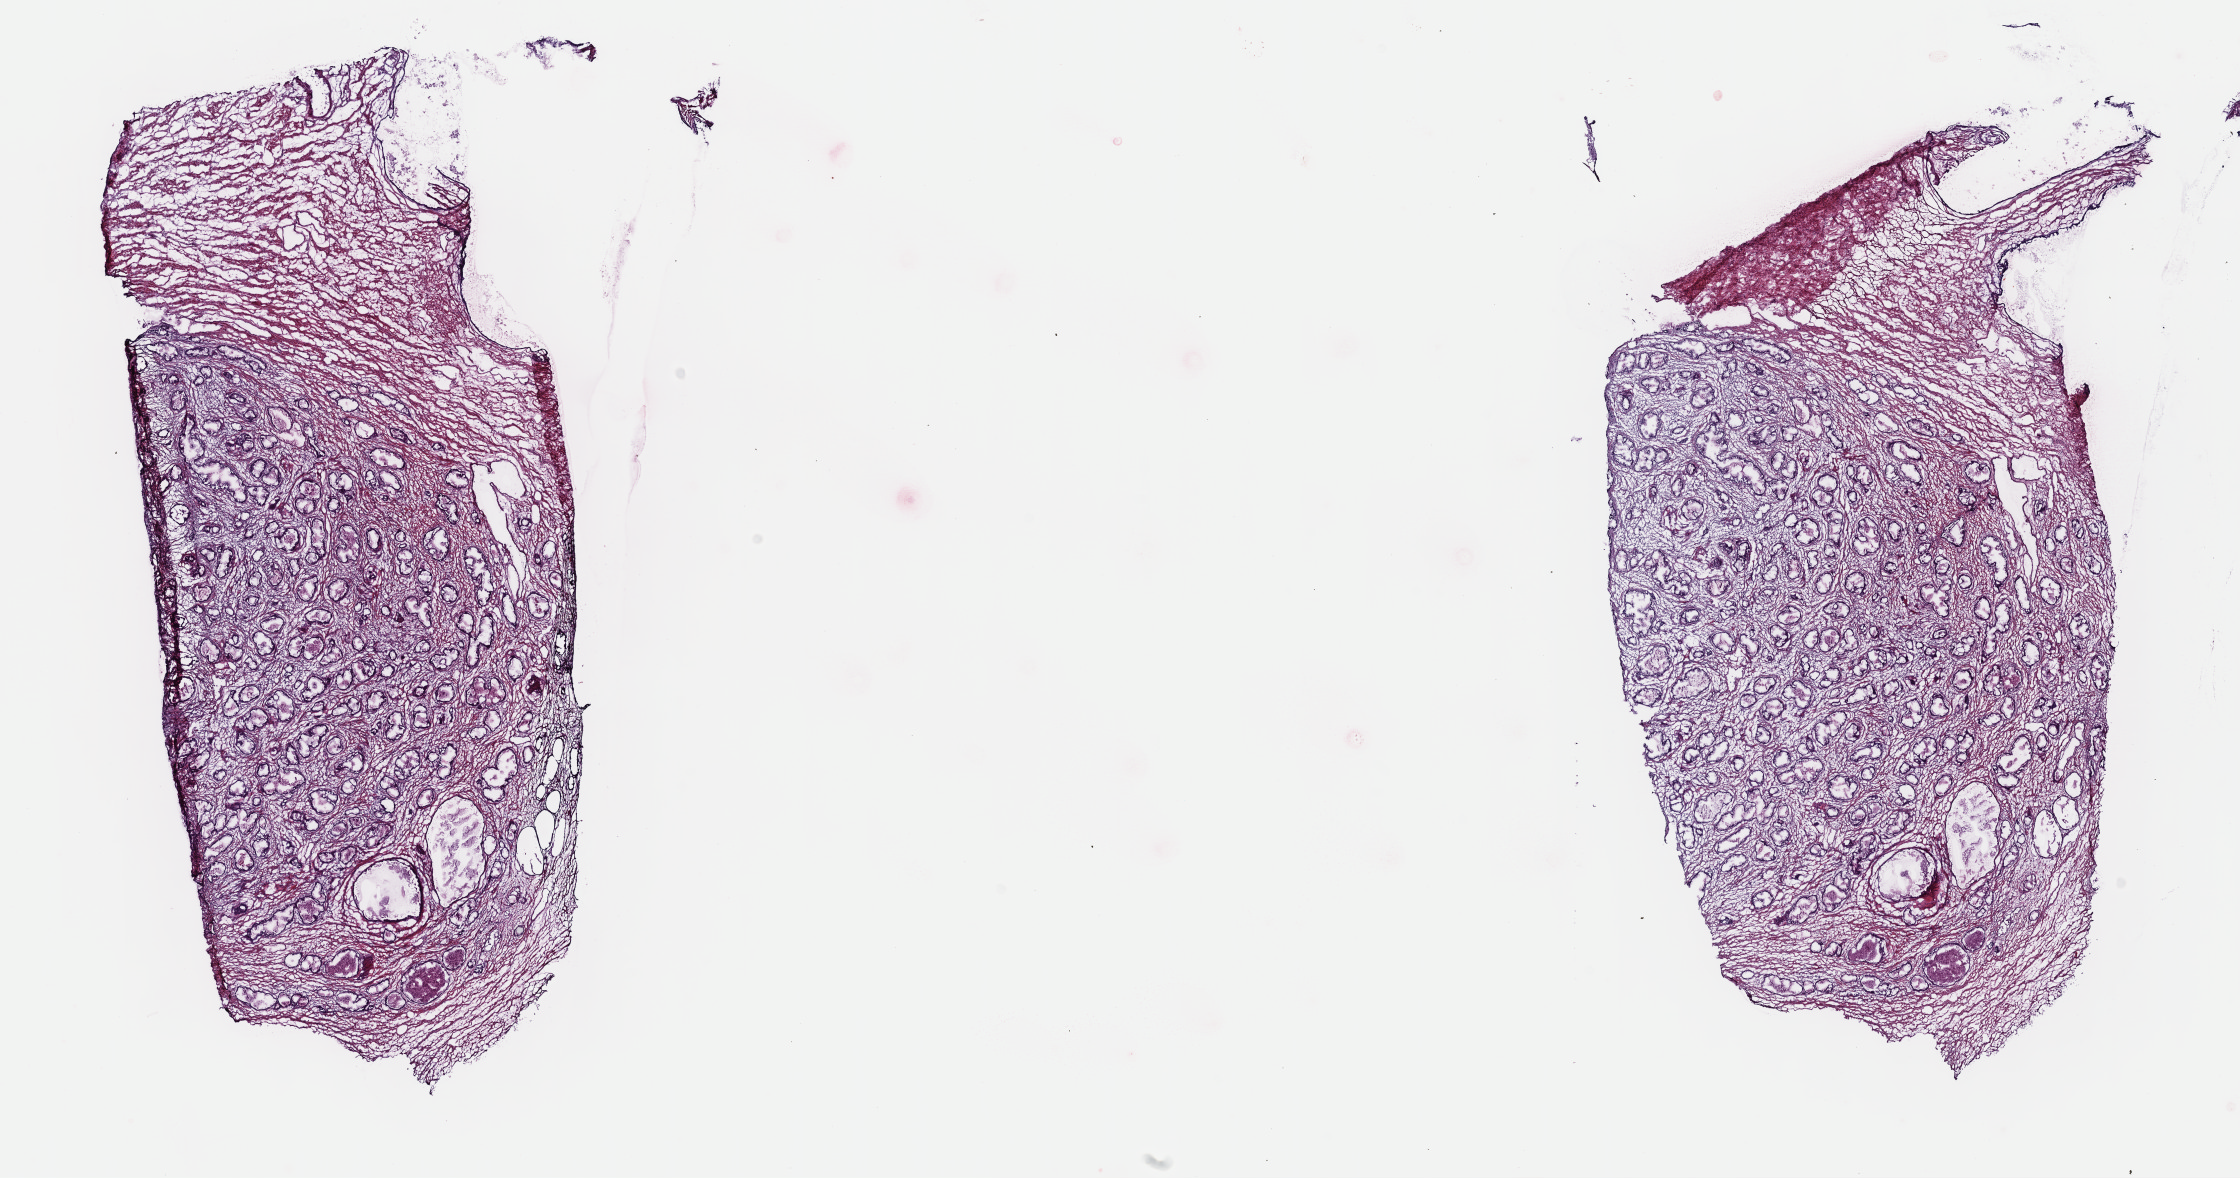
Digitized Hematoxylin and eosin (H&E) stained tissue section (whole slide) — low-resolution overview of the scanned area, about 18.1 x 9.5 mm, frozen section, sample: primary tumour, prostate. Male patient; age at initial diagnosis 61 years. Gleason score: 6 (3+3). Slide review estimates, as recorded: tumour cells 70%, tumour nuclei 70%, normal cells 5%, stromal cells 25%, necrosis 0%. Inflammatory infiltration, as recorded: lymphocyte infiltration 3%, monocyte infiltration 1%, neutrophil infiltration 2%.
Lymph nodes positive (case pathology): 0 of 18 examined. Histologic diagnosis: Adenocarcinoma, NOS (prostate gland). Laterality: bilateral.